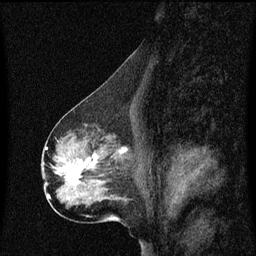
Breast MRI (dynamic contrast-enhanced), one sagittal slice; slice 30 of 60 in the series (ordered by position); dynamic contrast-enhanced series, image 2 of 3 at this slice position (ordered by acquisition); 1.5 T; TE 4.2 ms, TR 8.4 ms; 2 mm slice thickness; 256 × 256 image matrix. Female patient, age 50 years. Case-level facts recorded for this patient, not image findings: setting: breast cancer imaged before/during neoadjuvant chemotherapy; receptor status: HR-positive, HER2-negative.
Structures marked on this image (semi-automatically segmented with operator editing):
- analysis volume of interest (the breast-tissue region the enhancement analysis was run in; not a lesion): bounding box (x1, y1, x2, y2) in pixels: (55, 140, 133, 191)
- tumour enhancement mask (voxels above the 70 % enhancement threshold inside the analysis volume of interest): (60, 148, 127, 185)